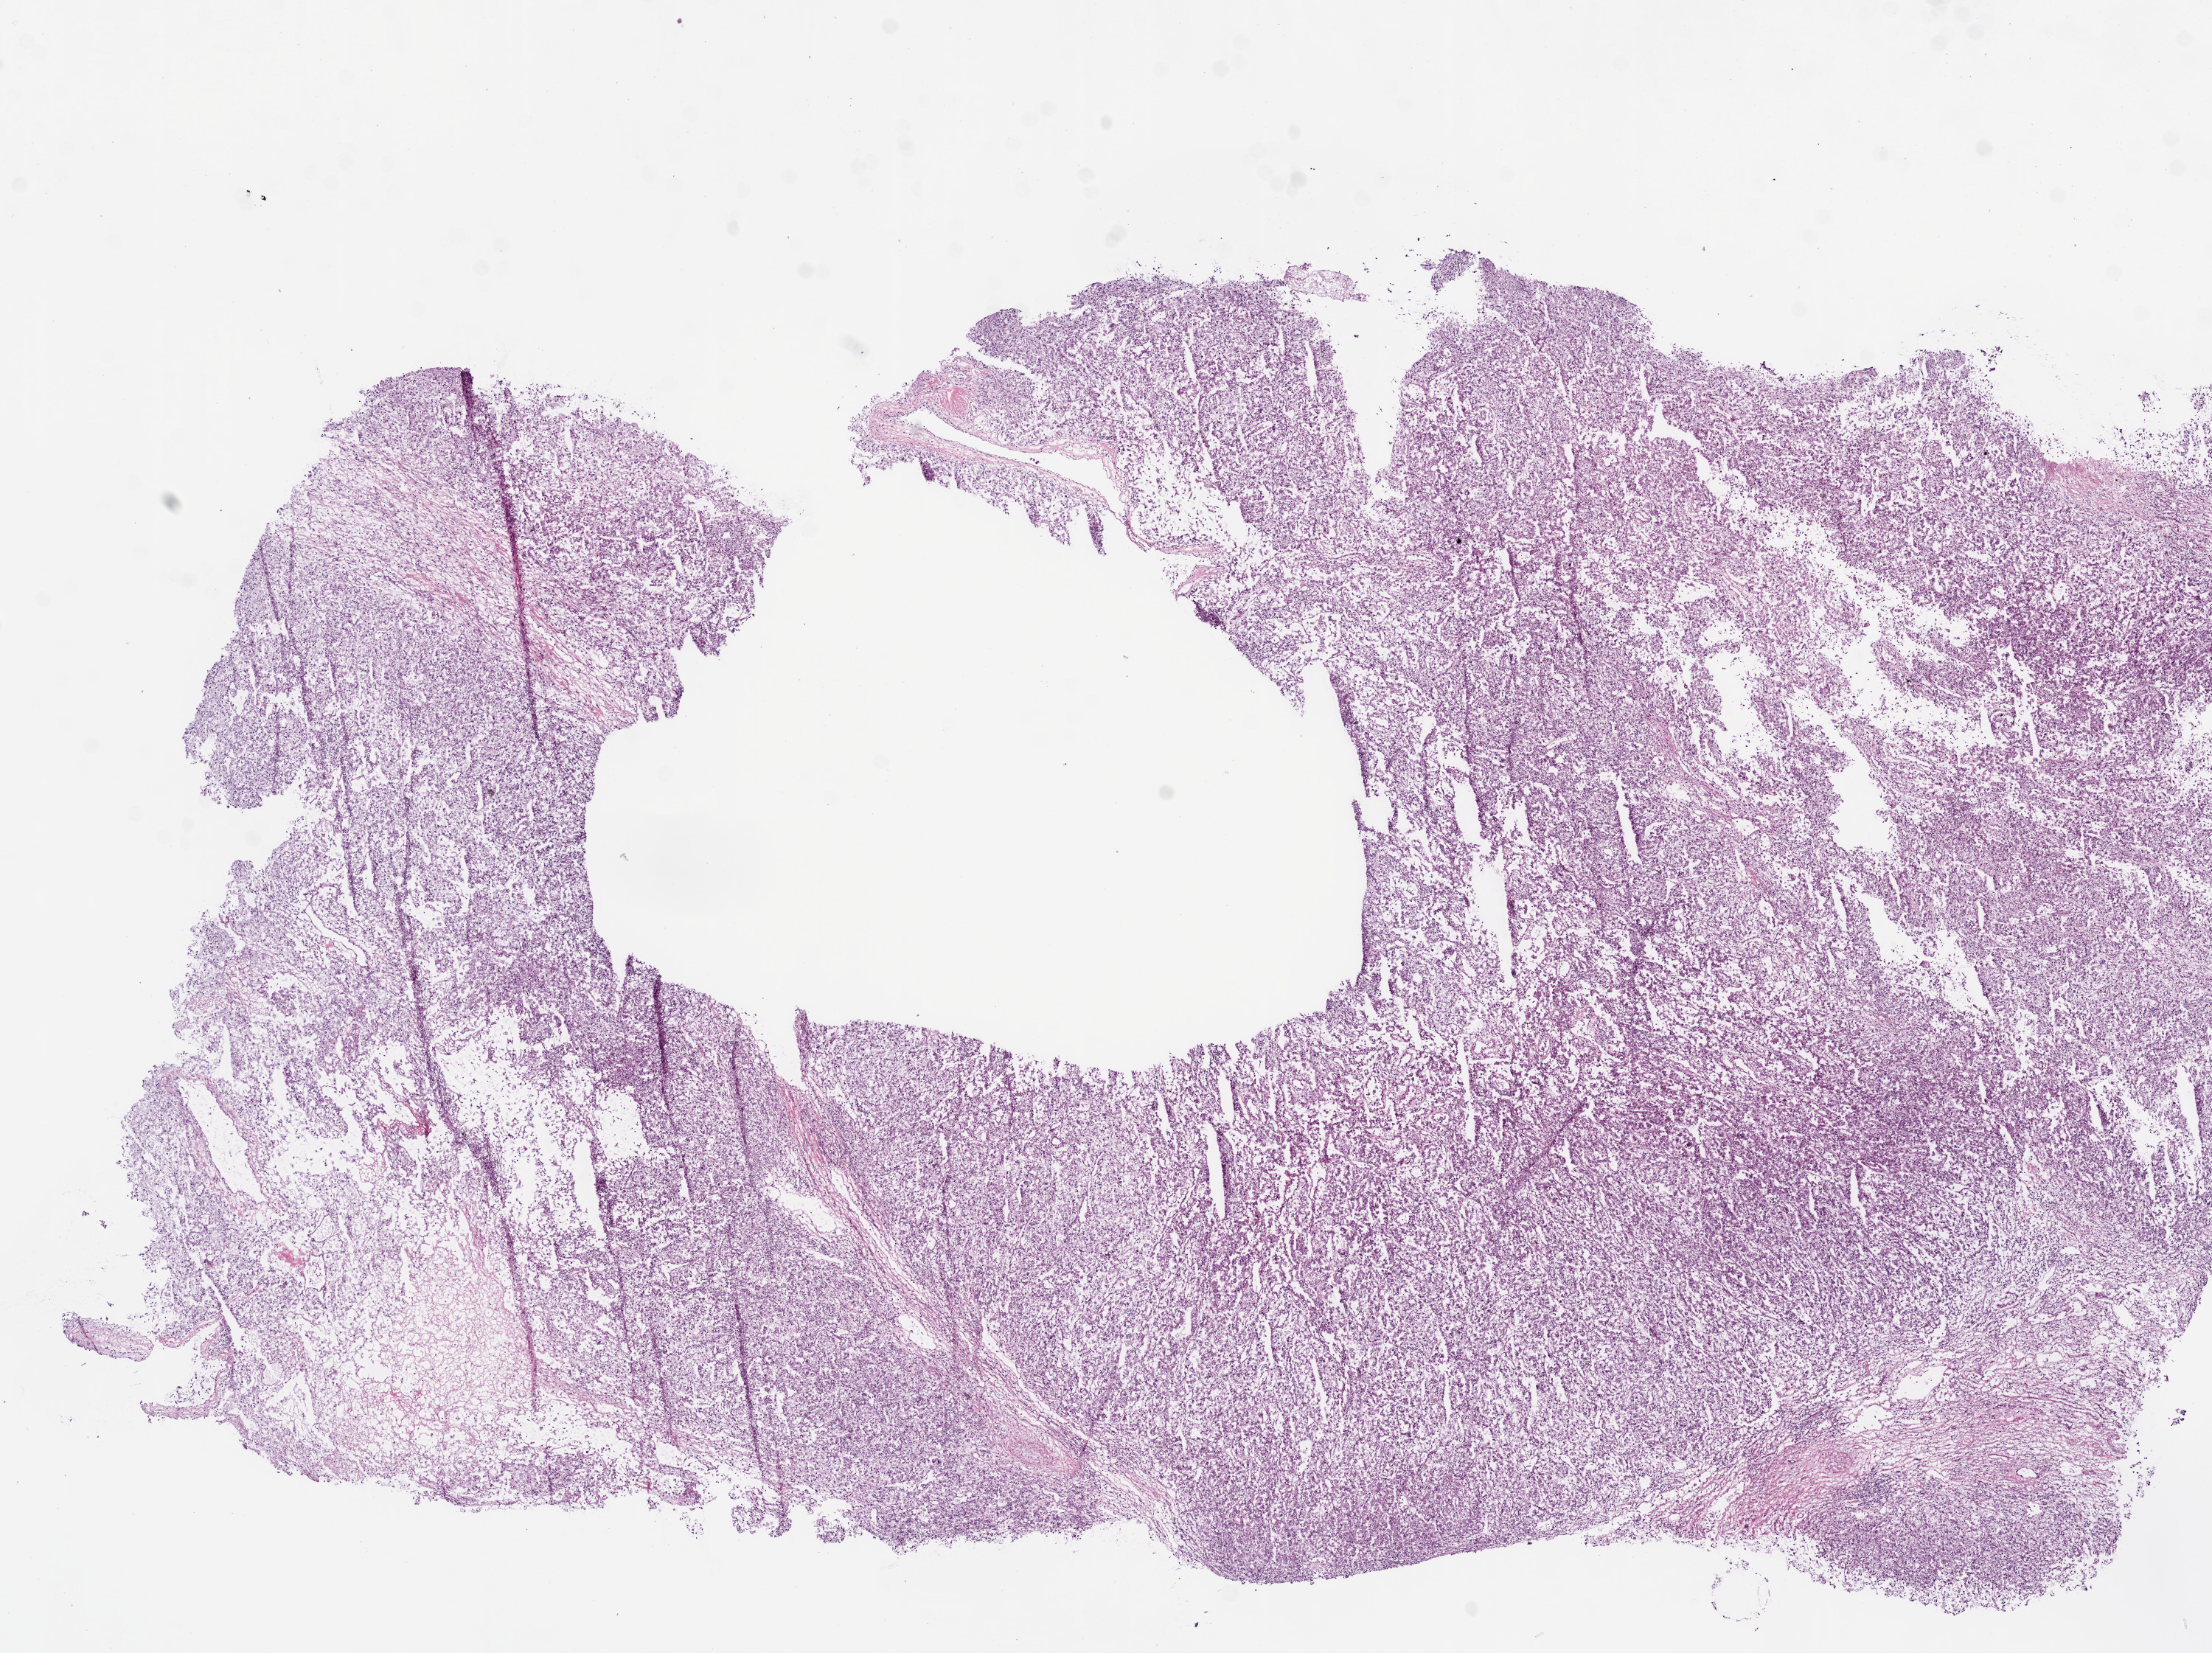
Whole-slide histology image, H&E-stained, low-resolution overview of the scanned area, about 12.0 x 9.0 mm (from a 20x scan), frozen section from the bottom of the tissue portion, sample: primary tumour, kidney. Patient: male, age at initial diagnosis 74 years. Histologic grade: G4 (undifferentiated). Composition of this section per pathologist review: tumour cells 100%, tumour nuclei 95%, normal cells 0%, stromal cells 0%, necrosis 0%.
• lymph nodes positive (case pathology): 0 of 30 examined
• histologic diagnosis: Clear cell adenocarcinoma, NOS